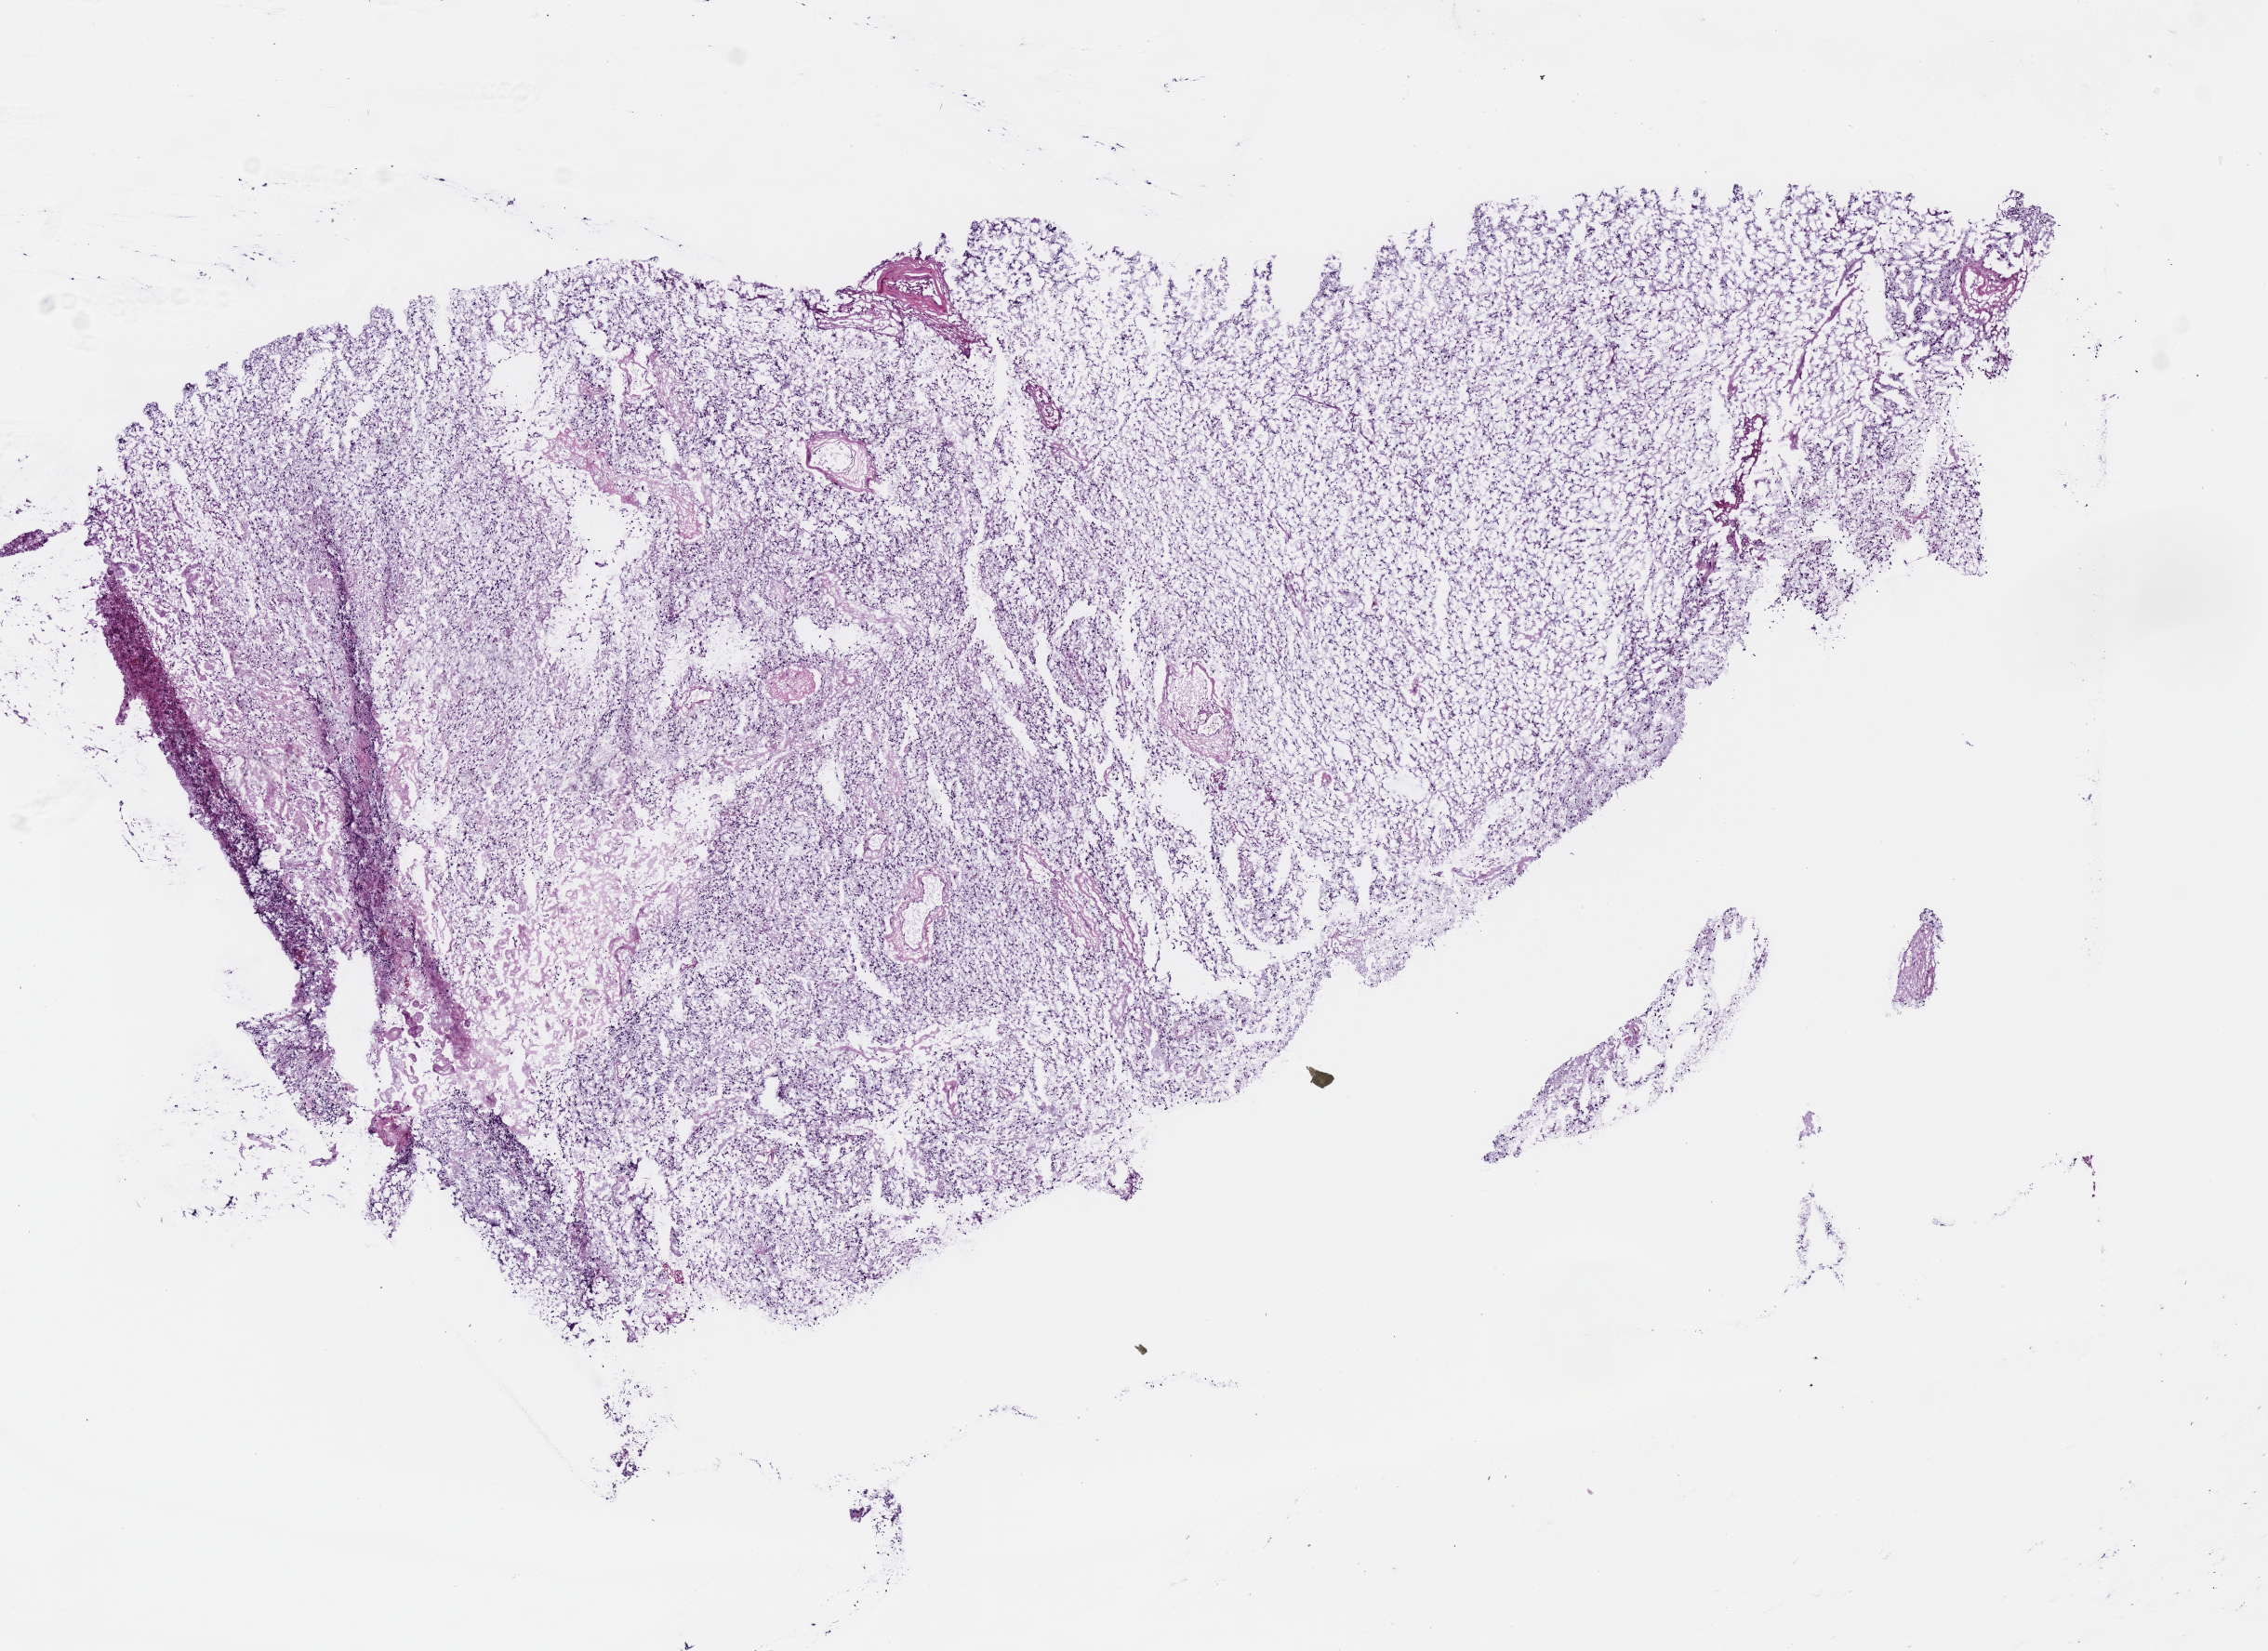
Digitized Hematoxylin and eosin (H&E) stained tissue section (whole slide), whole scanned area (about 9.6 x 7.0 mm, slide scanned at 40x) shown as a low-resolution overview; frozen section; brain, primary tumour sample. Patient: female, age at initial diagnosis 51 years. Histologic grade: G2 (moderately differentiated). Pathologist review of this section (percent, as recorded): tumour cells 95%, tumour nuclei 80%, normal cells 0%, stromal cells 5%, necrosis 0%.
Histologic diagnosis: Oligodendroglioma, NOS (cerebrum).